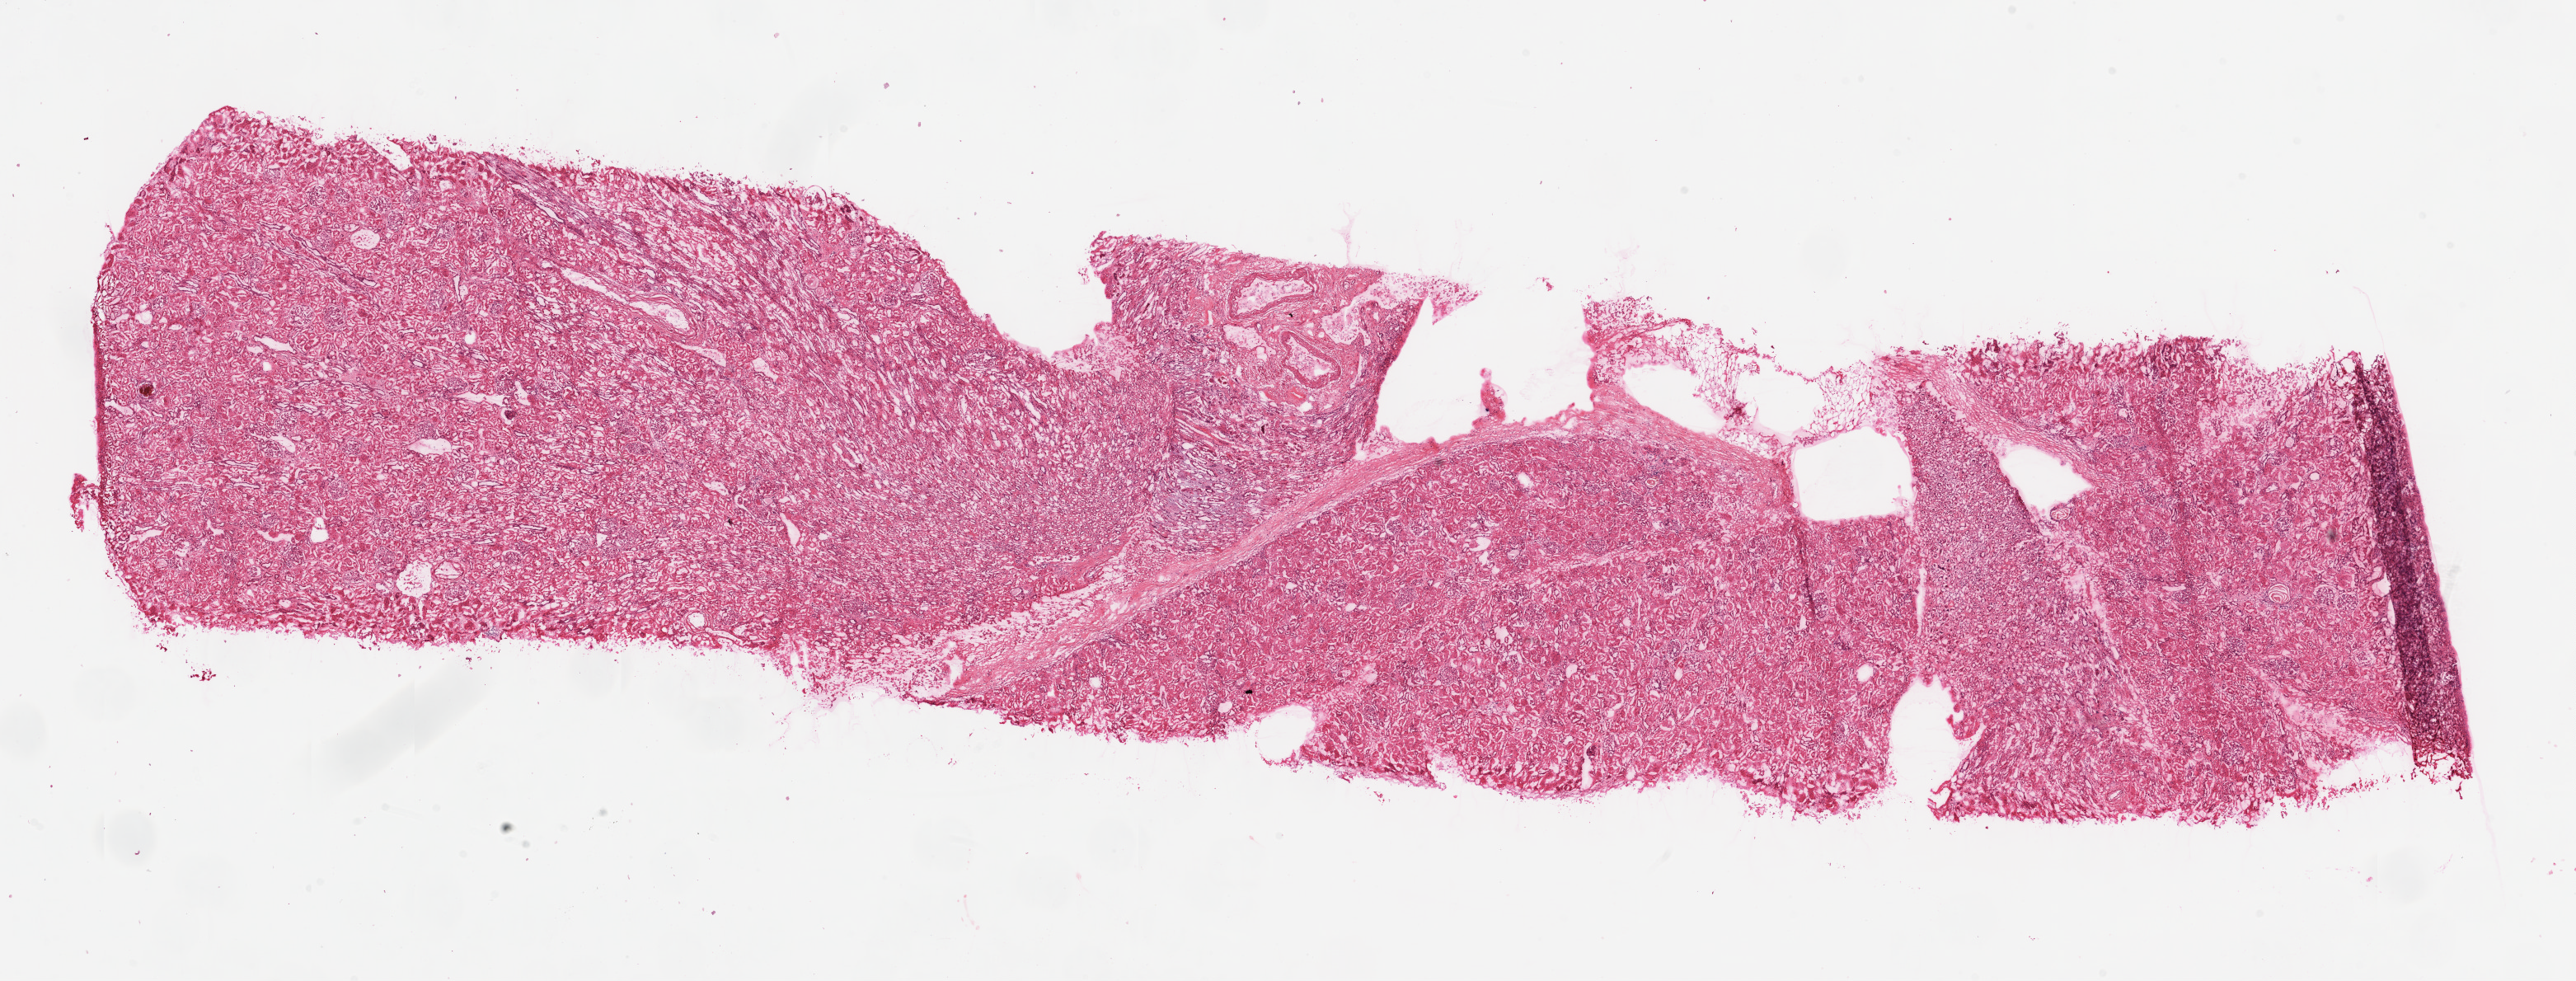
Hematoxylin and eosin (H&E) stained whole-slide image — shown as a low-resolution overview of the whole scanned area (about 25.1 x 9.5 mm); frozen section from the top of the tissue portion; sample: solid tissue normal (non-tumour tissue), kidney. Patient: male, age at initial diagnosis 57 years.
* this section: solid tissue normal sample (biorepository sample class)
* patient diagnosis: Clear cell adenocarcinoma, NOS